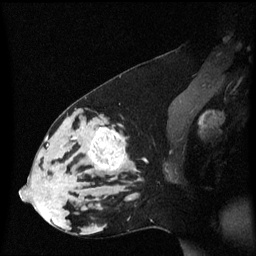
Breast MRI (dynamic contrast-enhanced), one sagittal slice. Position 31 of 60 along the scan axis. Dynamic contrast-enhanced series, image 2 of 3 at this slice position (ordered by acquisition). 1.5 T. TE 4.2 ms, TR 8.4 ms. 2 mm slice thickness. 256 × 256 image matrix, field of view 210 × 210 mm. Female patient, age 33 years. Case-level facts recorded for this patient, not image findings: setting: breast cancer imaged before/during neoadjuvant chemotherapy; receptor status: triple-negative.
Structures marked on this image (semi-automatic segmentation, software-assisted and operator-edited):
- analysis volume of interest (the breast-tissue region the enhancement analysis was run in; not a lesion): box from (x=44, y=123) to (x=138, y=189) px
- tumour enhancement mask (voxels above the 70 % enhancement threshold inside the analysis volume of interest): (x=88, y=128)–(x=127, y=172)